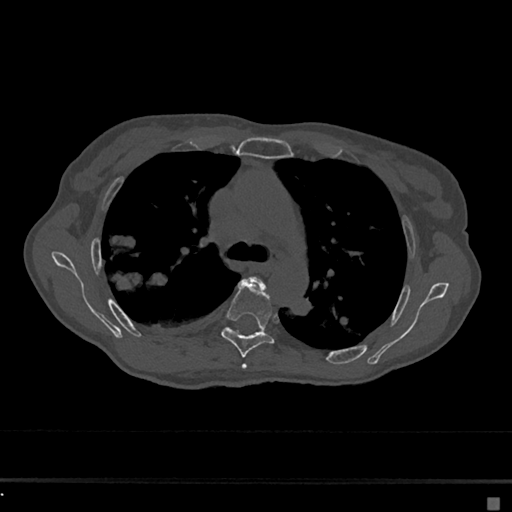
CT including the spine, one axial slice. Slice 462 of 797 in the series (ordered by position). Reconstruction kernel Br40s/3. 120 kVp. Bone window (W 1800 / L 400 HU). 0.5 mm slice thickness. 512 × 512 image matrix, field of view 360 × 360 mm. Patient: female, 68 years. From the clinical record (not read from this slice): primary cancer: renal.
Annotated regions visible in this slice (semi-automatic segmentation, software-assisted and operator-edited):
- T4 vertebra: box from (x=241, y=276) to (x=266, y=370) px
- T5 vertebra: (x=220, y=280)–(x=275, y=358)